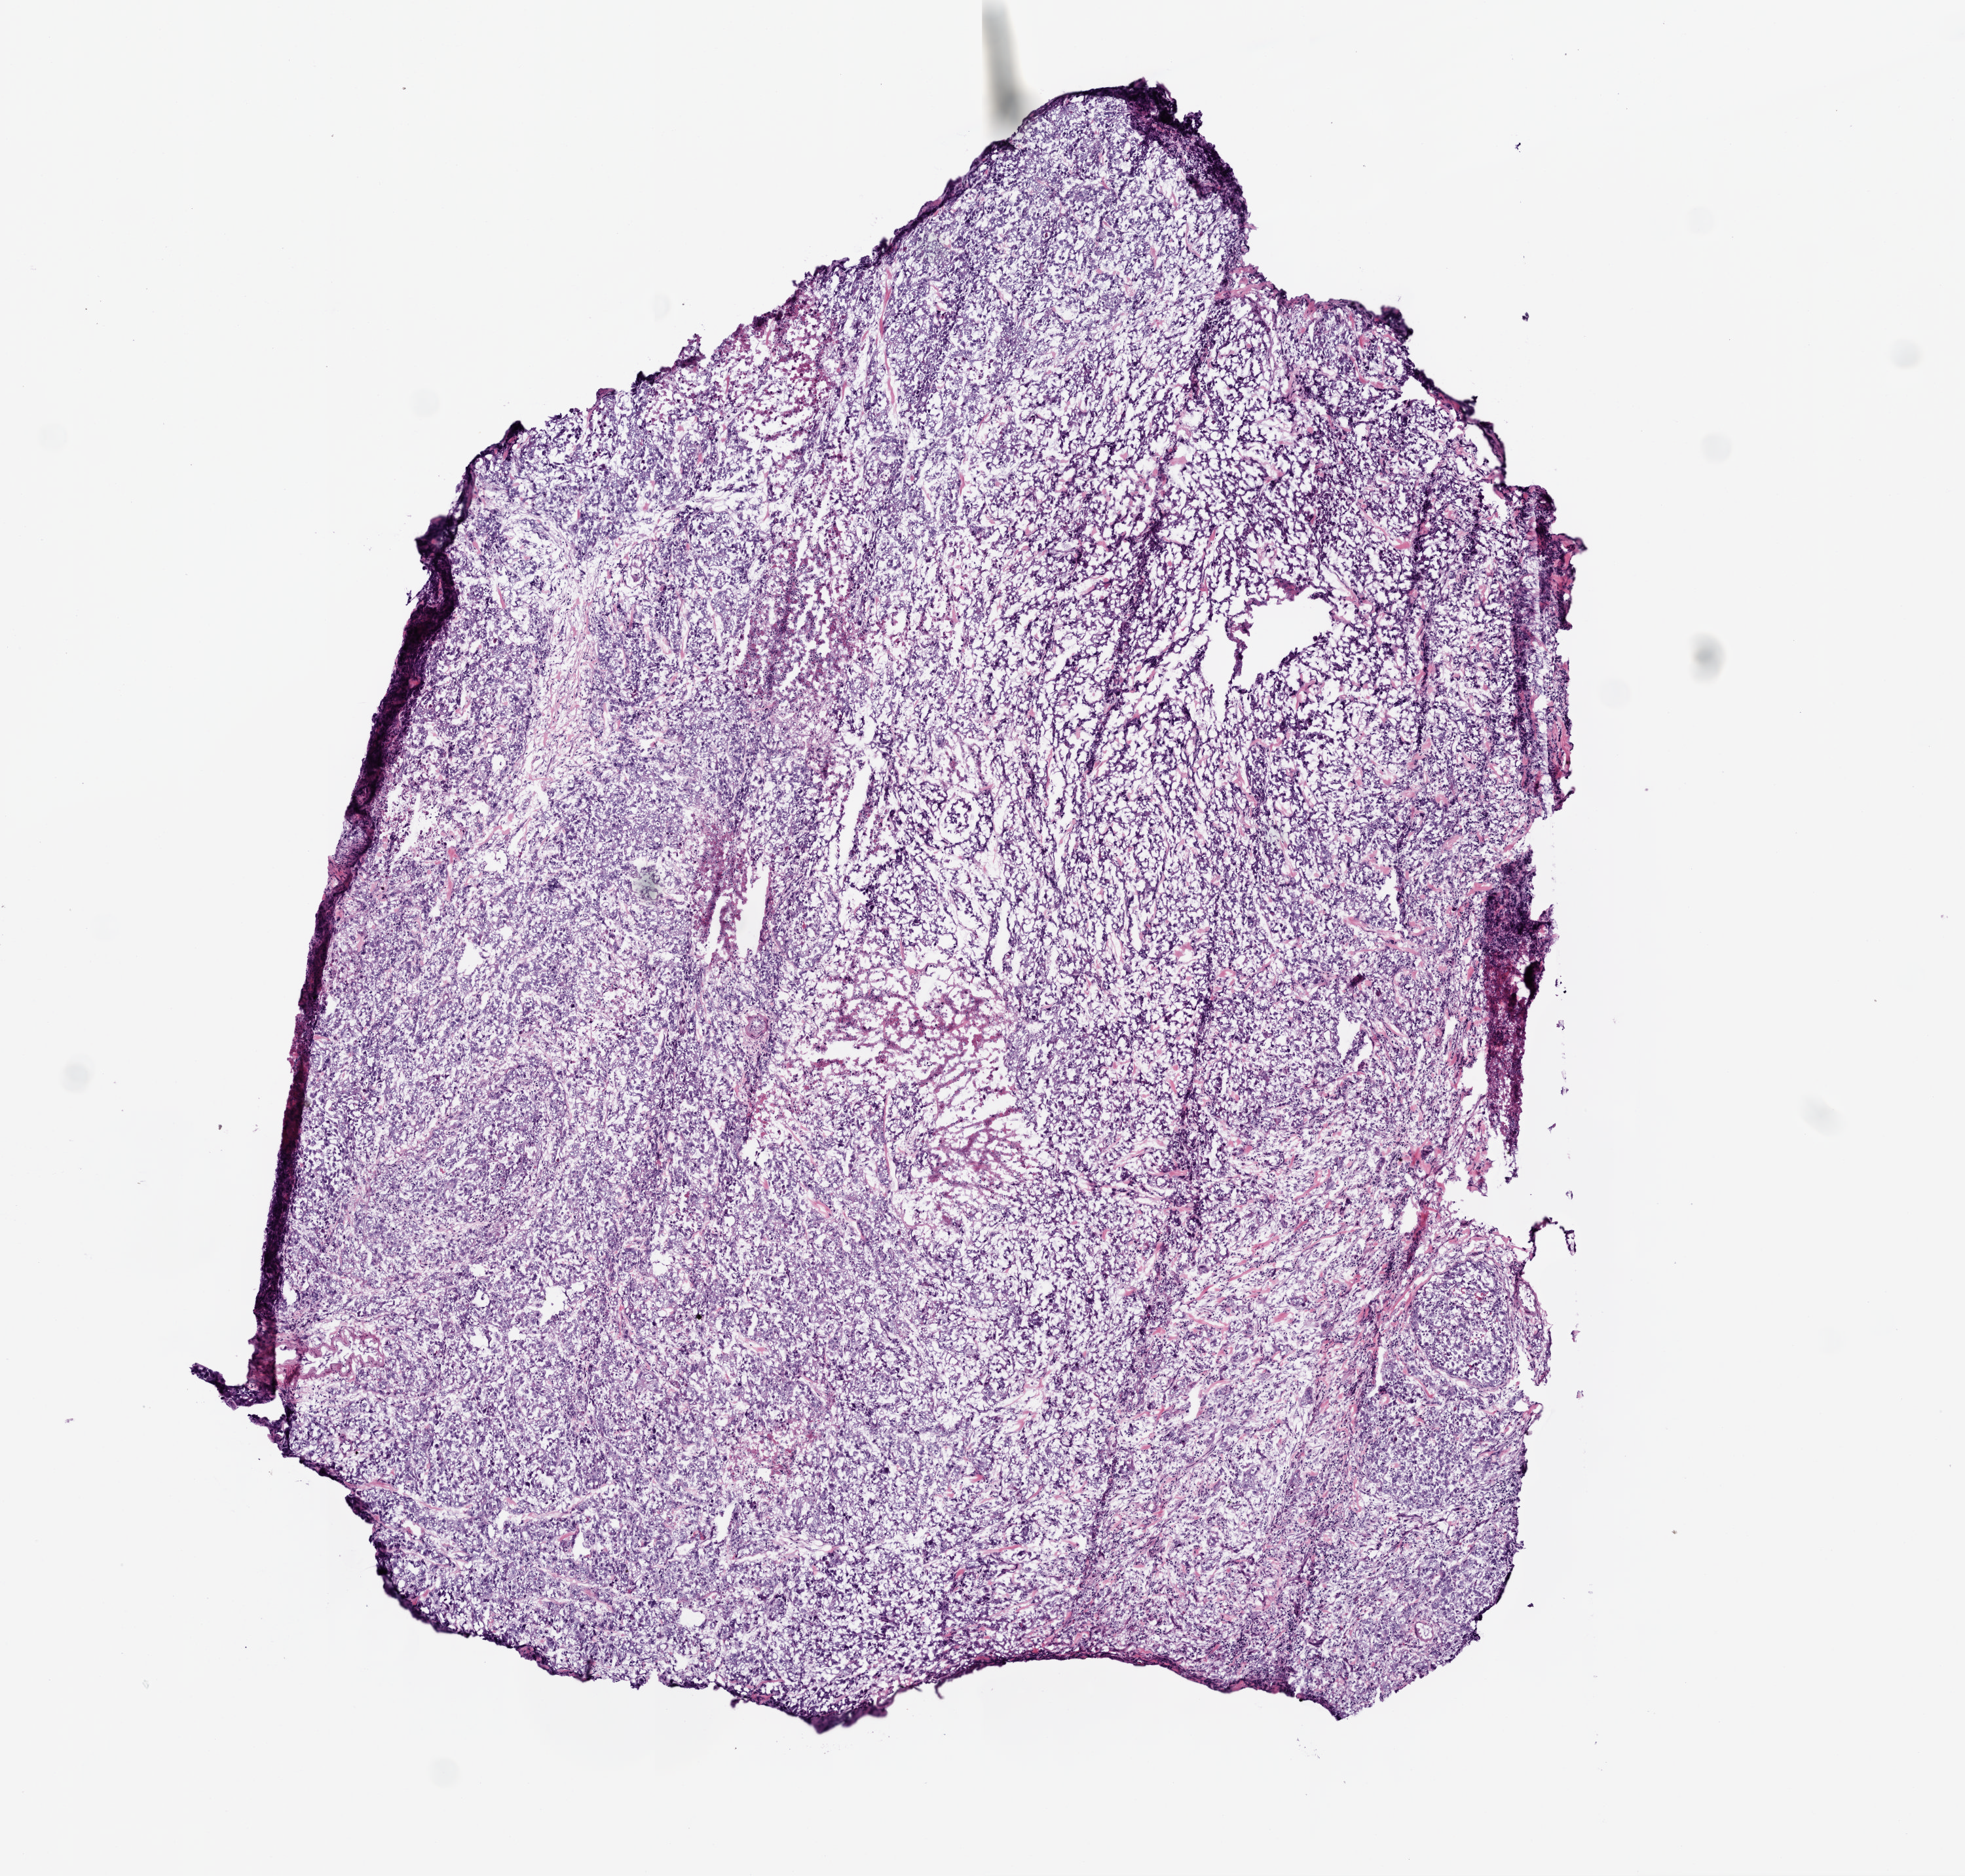
Digitized Hematoxylin and eosin (H&E) stained tissue section (whole slide), a low-resolution overview of the entire scanned area, about 6.0 x 5.7 mm (from a 20x scan), frozen section from the top of the tissue portion, primary tumour sample from the stomach. Female, age 68 years at initial diagnosis. Histologic grade: G3 (poorly differentiated). Slide review estimates, as recorded: tumour cells 87%, tumour nuclei 80%, normal cells 0%, stromal cells 5%, necrosis 8%.
AJCC pathologic stage: IV. Pathologic diagnosis: Adenocarcinoma, intestinal type (body of stomach). Lymph nodes positive (case pathology): 18 of 24 examined.